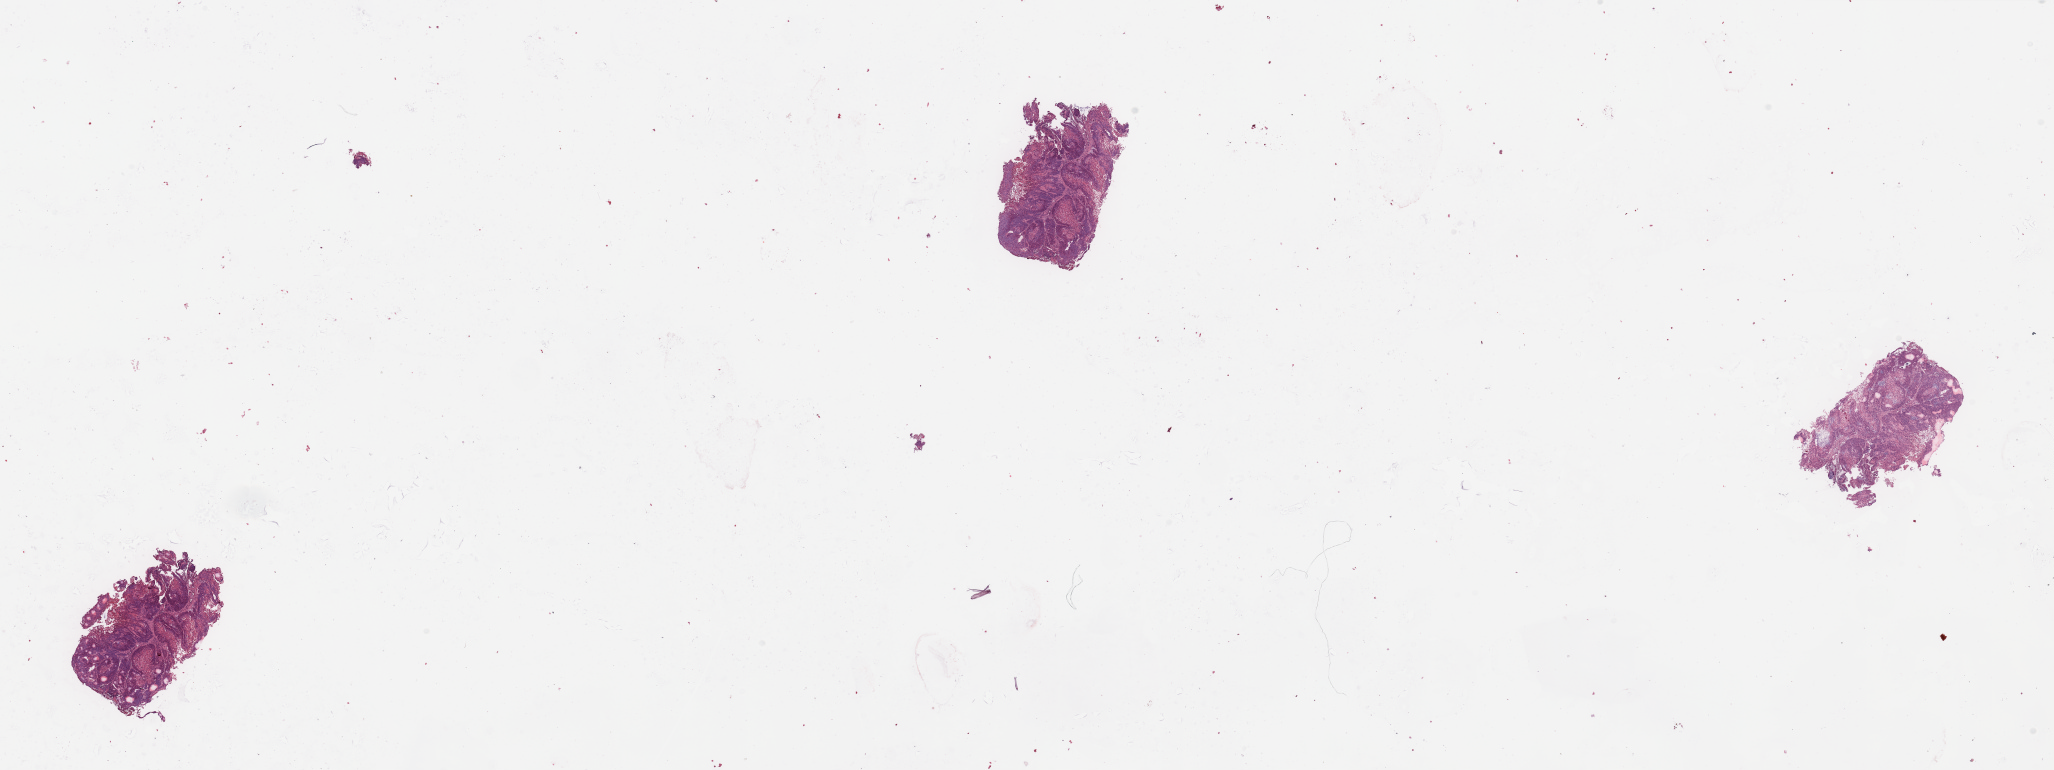
H&E-stained whole-slide image — shown as a low-resolution overview of the whole scanned area (about 32.5 x 12.2 mm, from a 20x scan). Tumour tissue sample, sampled site: larynx. Female, 68 y/o. Pathologist review of this section (percent, as recorded): tumour nuclei 80%, necrosis 10%.
Diagnosis: Squamous cell carcinoma, NOS (larynx, NOS).